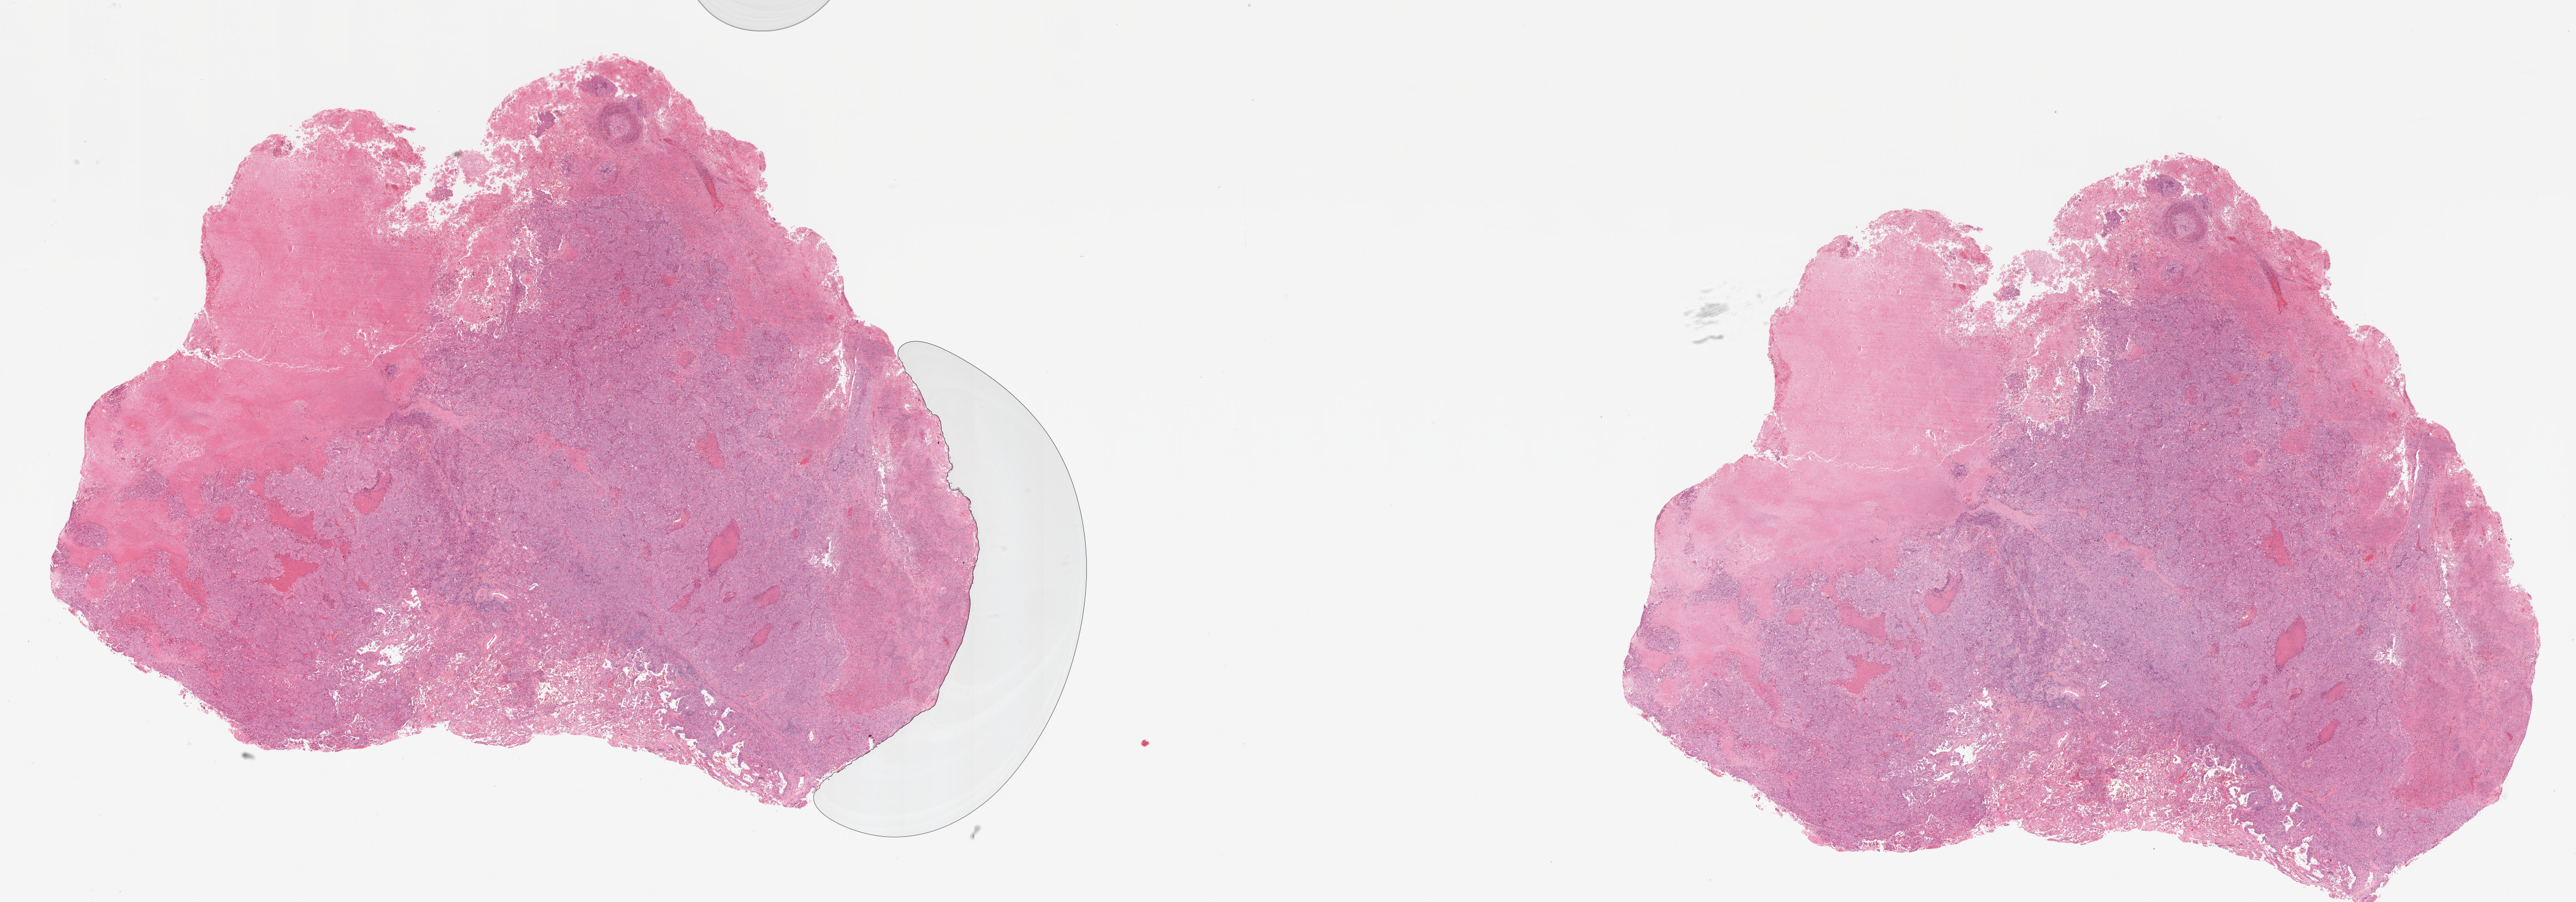
H&E whole-slide image — low-resolution overview of the scanned area, about 37.0 x 13.0 mm (acquisition: 20x scan); formalin-fixed paraffin-embedded (FFPE) diagnostic section; primary tumour sample from the lung. Patient sex: female.
Pathologic diagnosis: Papillary adenocarcinoma, NOS (upper lobe, lung).